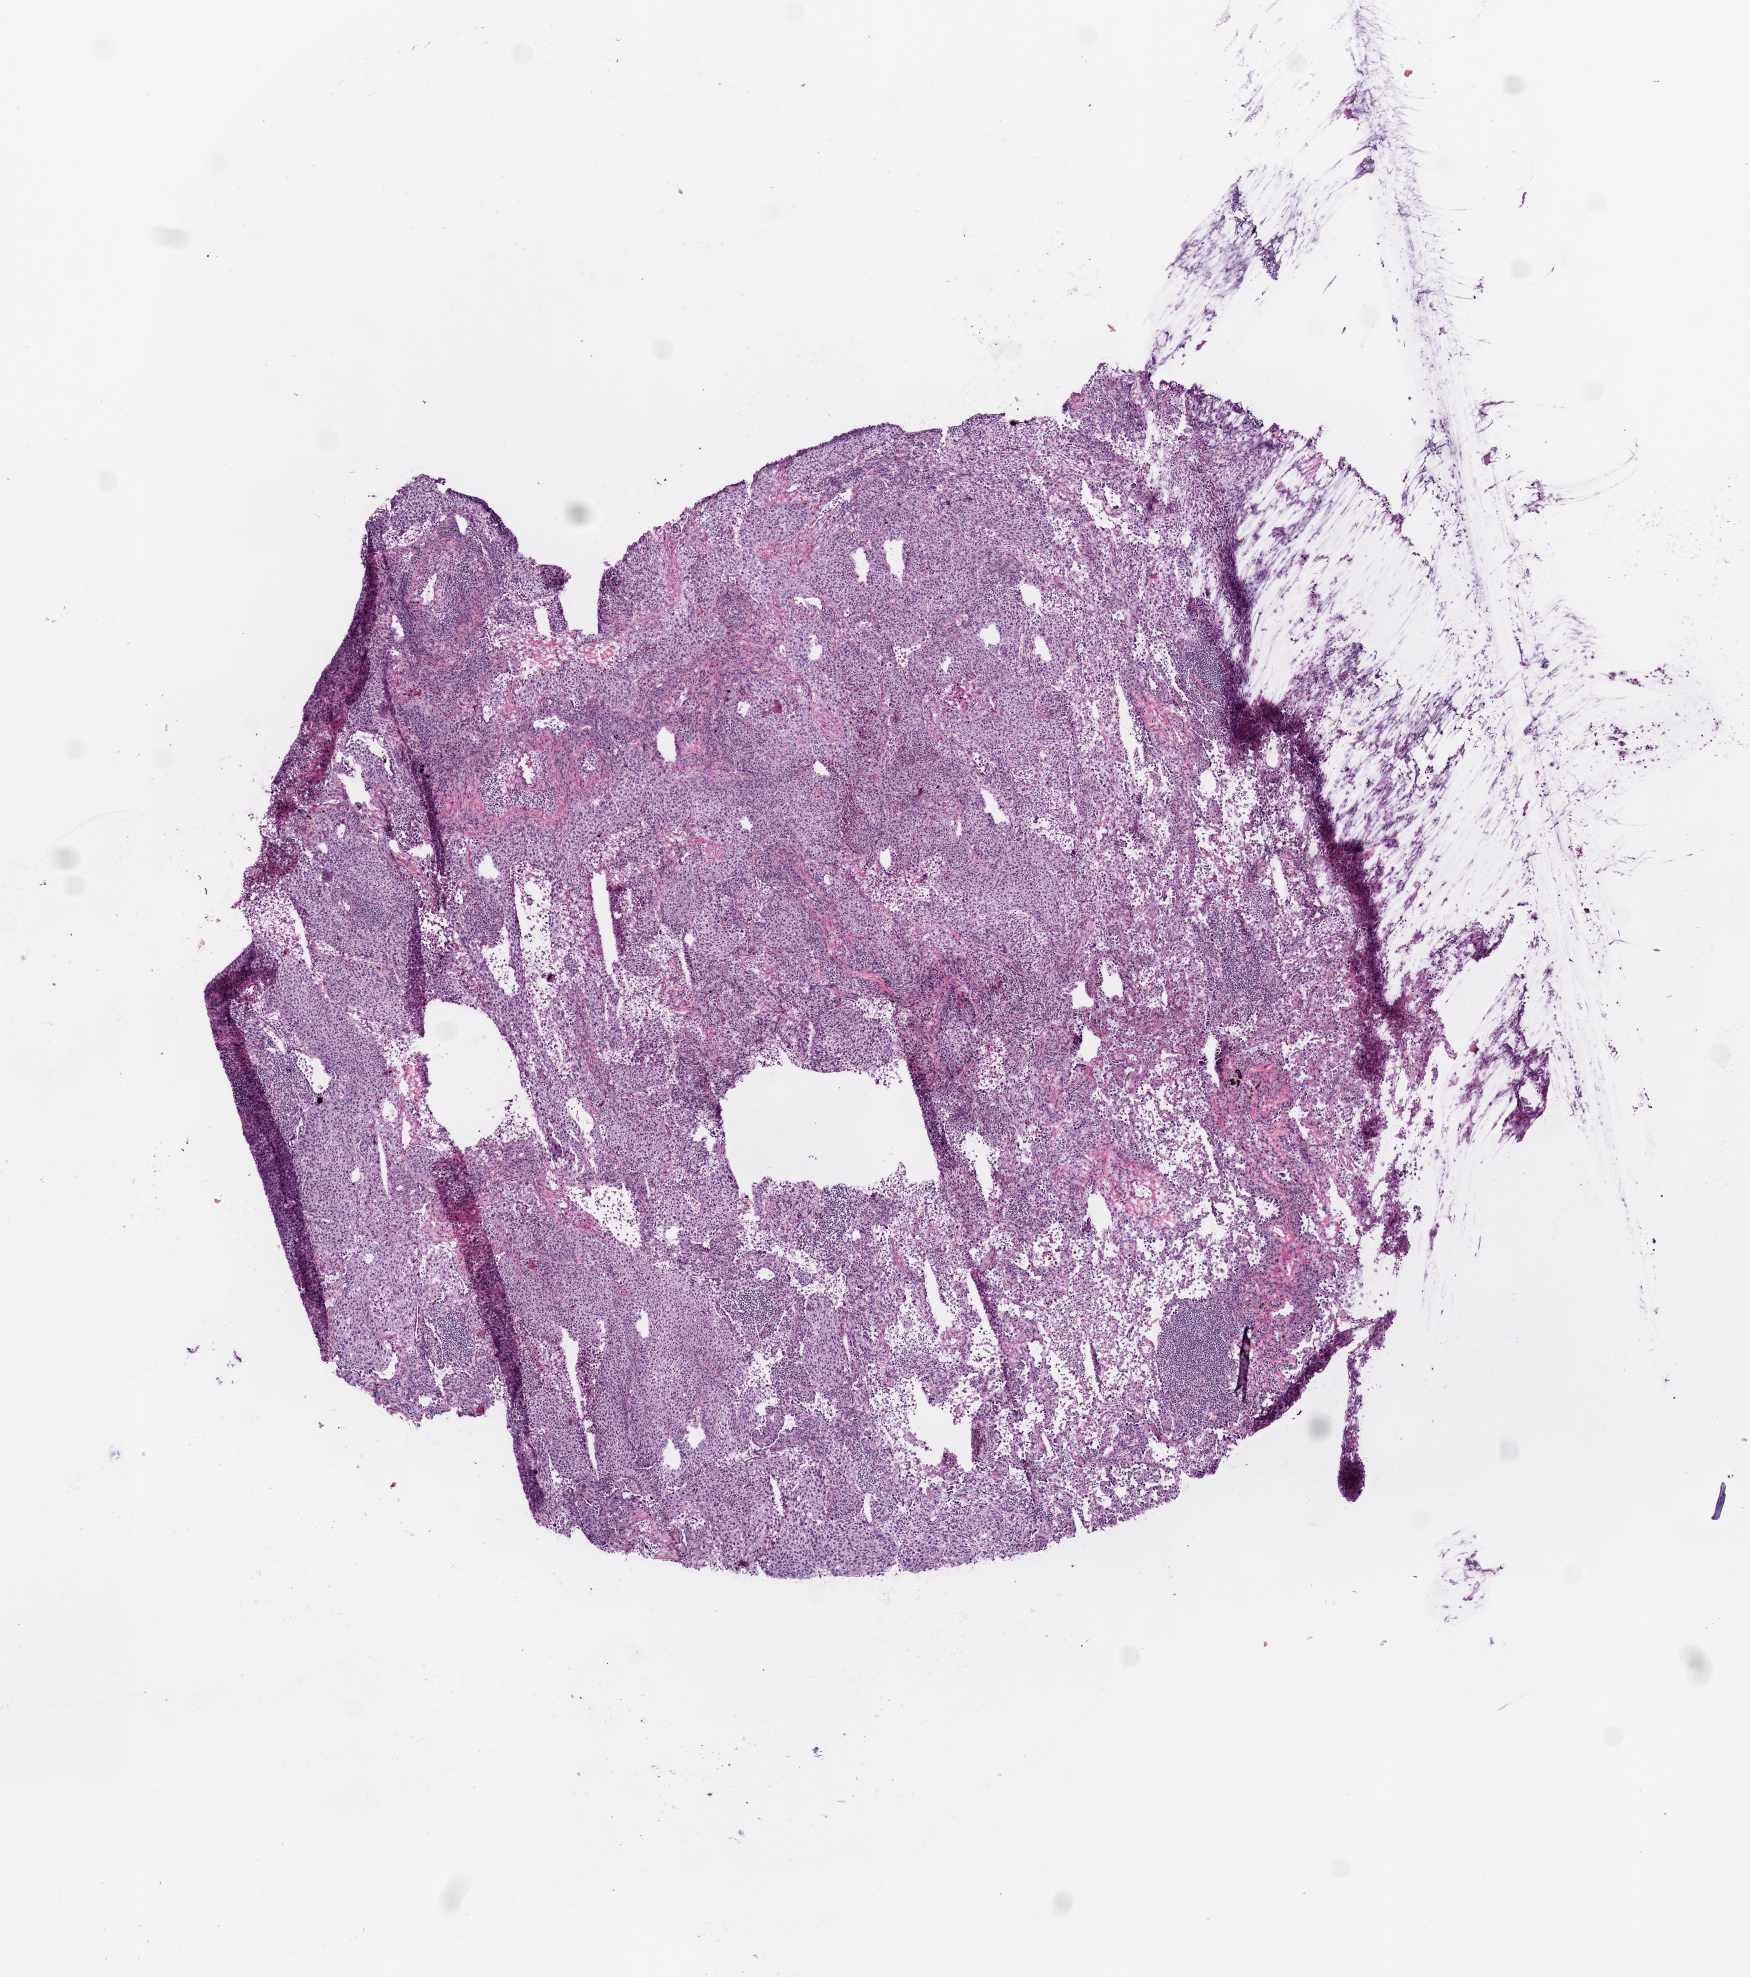
Whole-slide histology image, H&E-stained — shown as a low-resolution overview of the whole scanned area (about 7.0 x 7.9 mm), frozen section, primary tumour sample from the lung. Patient: male, age at initial diagnosis 60 years. Pathologist review of this section (percent, as recorded): tumour cells 85%, tumour nuclei 75%, normal cells 5%, stromal cells 5%, necrosis 5%. Infiltration values recorded for this section: lymphocyte infiltration 15%, monocyte infiltration 2%, neutrophil infiltration 0%.
Pathologic diagnosis: Squamous cell carcinoma, NOS. AJCC pathologic stage: IIB (6th edition). Laterality: right.